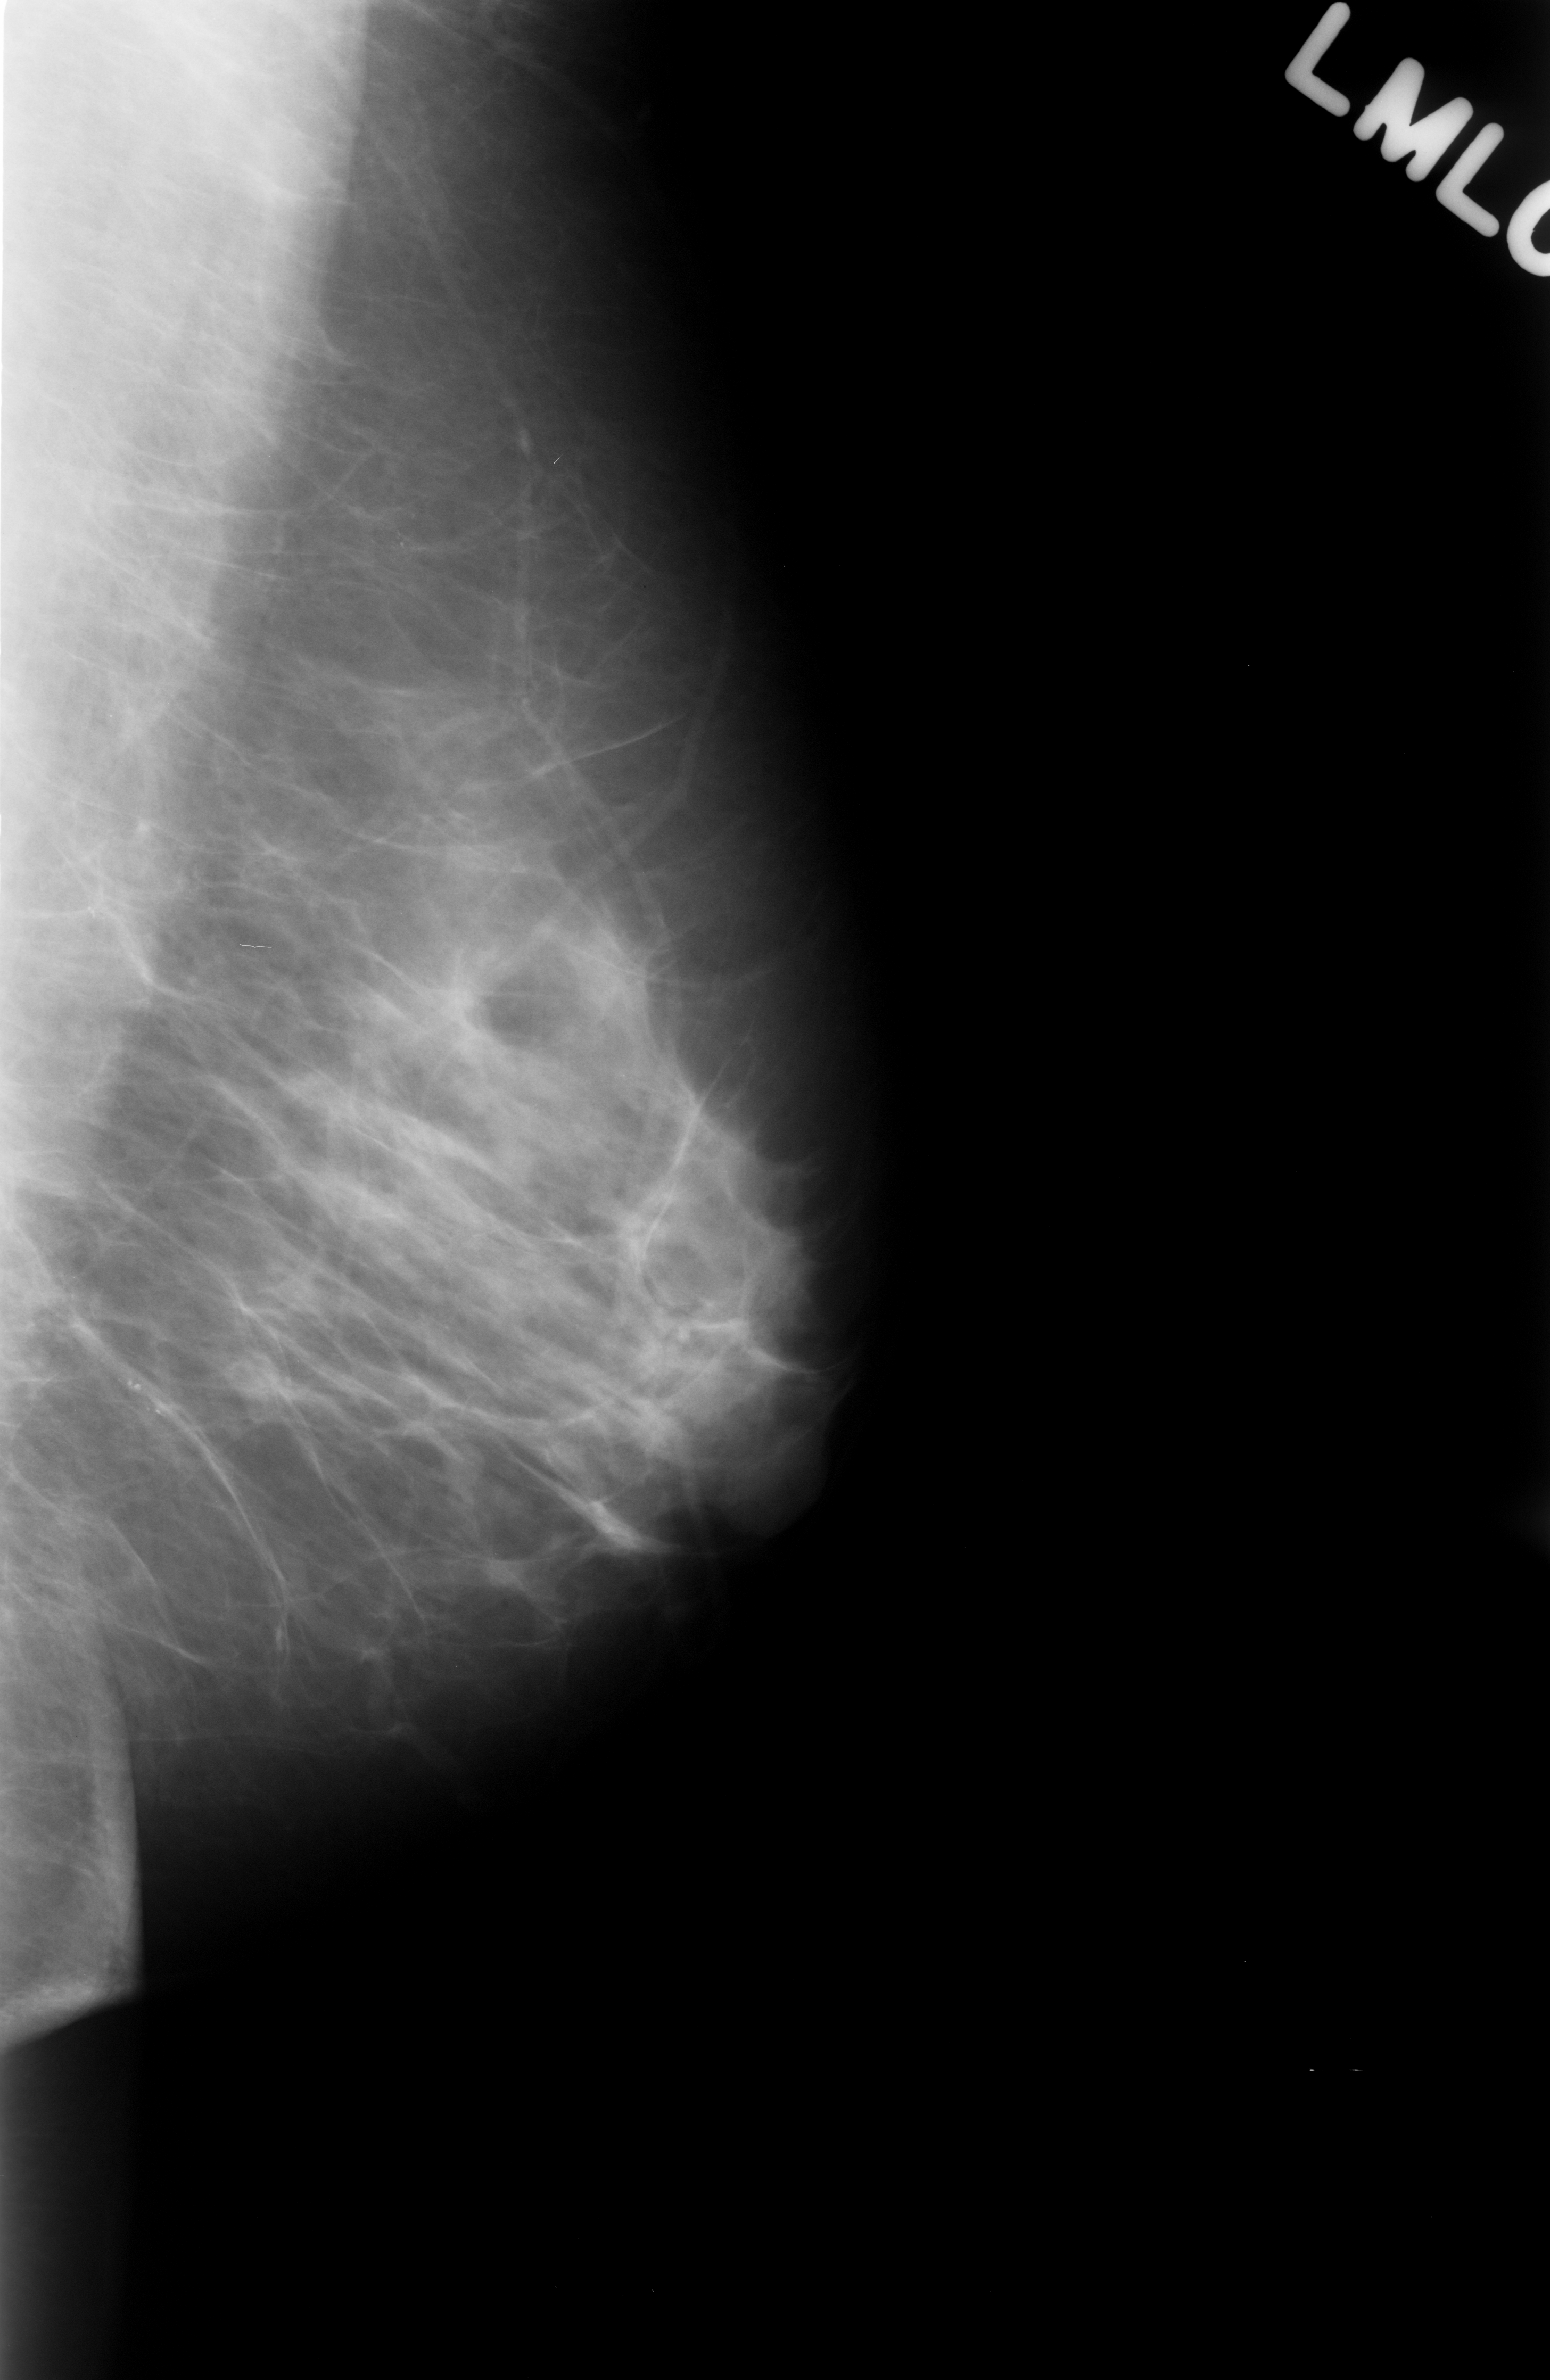
Scanned film-screen mammogram. Left breast. MLO view. 1550 × 2380 image matrix.
Expert-marked regions of interest on this film, with their recorded descriptors:
- calcifications, morphology punctate, distribution clustered; BI-RADS assessment category 4; subtlety rating 4 on a 1 (subtle) to 5 (obvious) scale; pathology result (as recorded, not read from the image): benign: bounding box (x1, y1, x2, y2) in pixels: (34, 1255, 265, 1478)